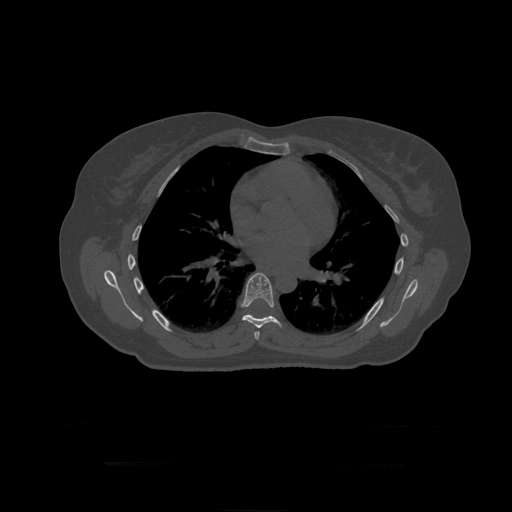
CT including the spine, one axial slice; position 282 of 399 along the scan axis; bone window (W 1800 / L 400 HU); 512 × 512 image matrix, field of view 450 × 450 mm. Patient age 41 years. Case-level facts recorded for this patient, not image findings: primary cancer: breast.
Structures marked on this image (semi-automatically segmented with operator editing):
- T7 vertebra: bounding box [x1, y1, x2, y2] px = [254, 331, 260, 340]
- T8 vertebra: [241, 273, 283, 329]